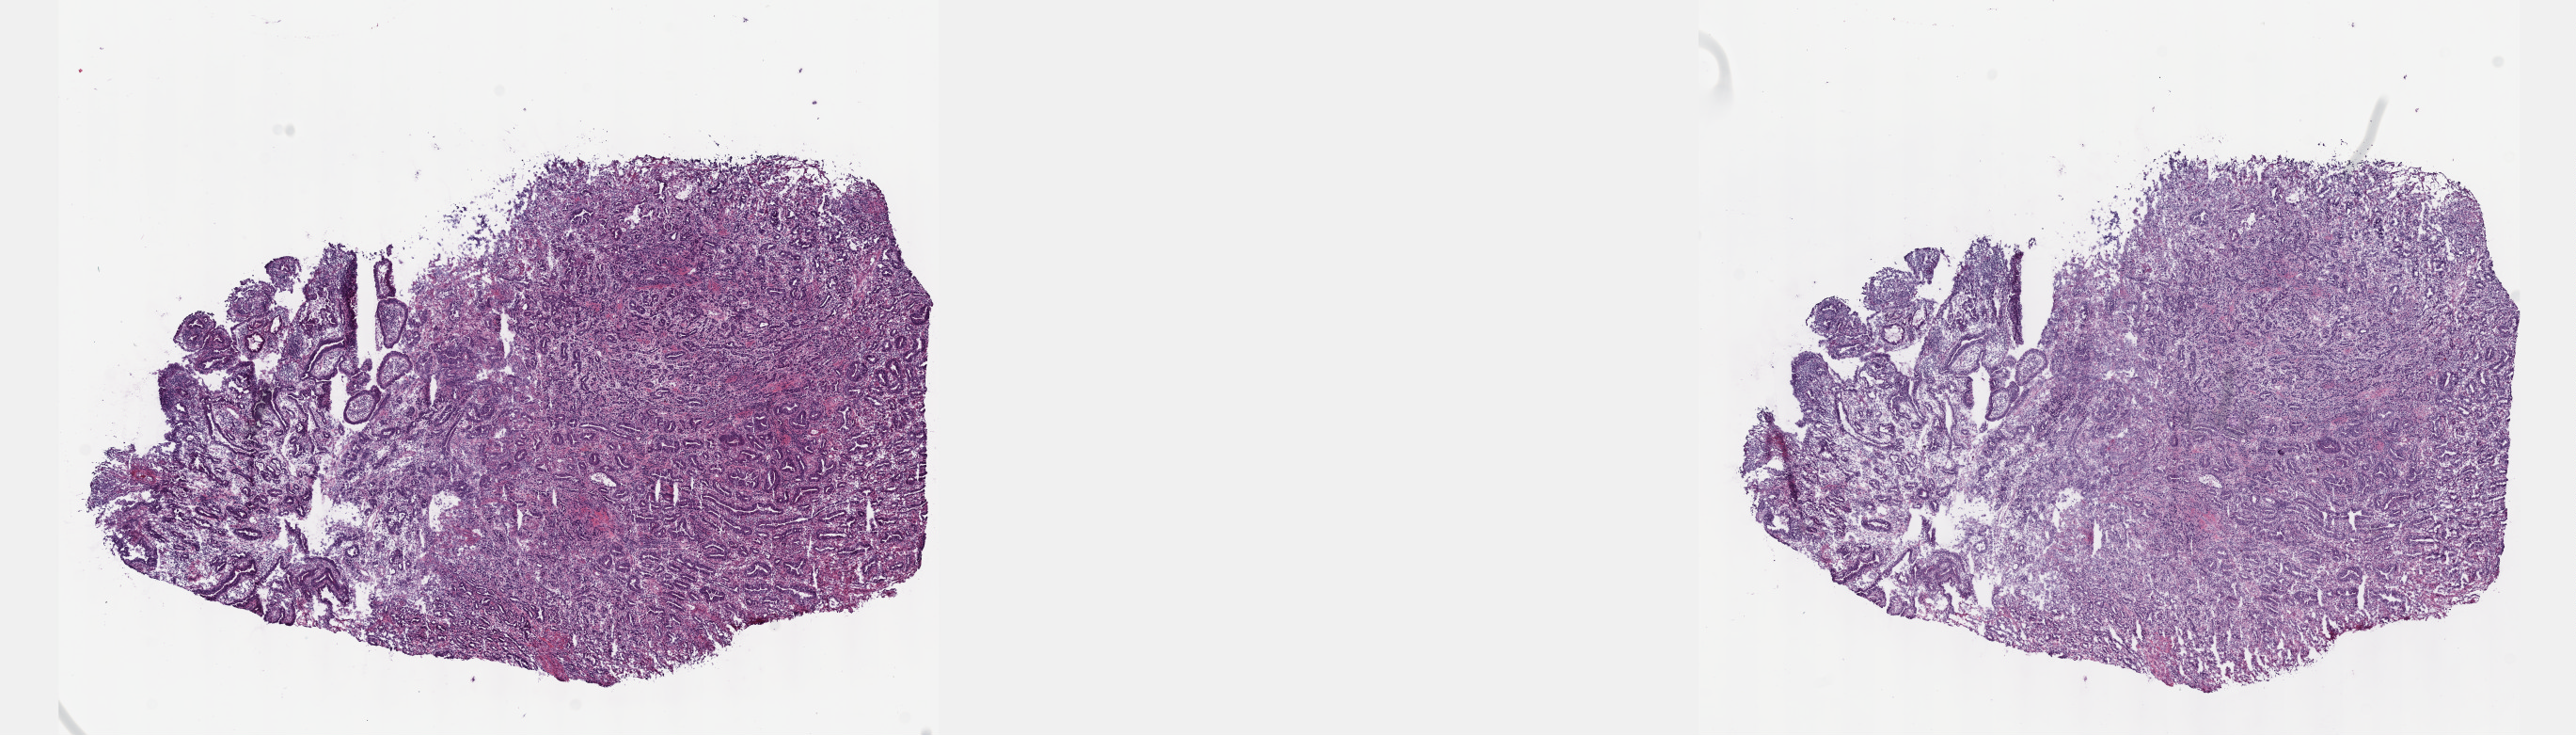
Whole-slide histology image, H&E-stained — a low-resolution overview of the entire scanned area, about 22.1 x 6.3 mm (from a 40x scan), frozen section from the top of the tissue portion, primary tumour sample from the esophagus. Patient: male, age at initial diagnosis 54 years. Histologic grade: GX (grade cannot be assessed). Composition of this section per pathologist review: tumour cells 85%, tumour nuclei 90%, normal cells 0%, stromal cells 15%, necrosis 0%. Inflammatory infiltration, as recorded: lymphocyte infiltration 6%, monocyte infiltration 6%, neutrophil infiltration 0%.
Histologic diagnosis: Adenocarcinoma, NOS (lower third of esophagus). AJCC pathologic stage: IV. TNM: T1 N0 M1.